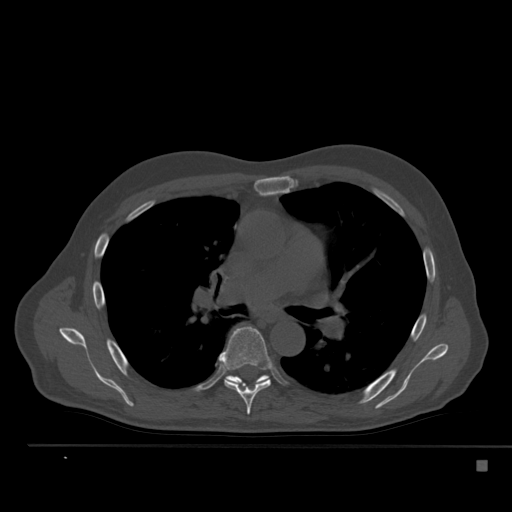
CT including the spine, one axial slice. Position 342 of 517 along the scan axis. Reconstruction kernel Br40s. 120 kVp. Bone window (W 1800 / L 400 HU). 512 × 512 image matrix. Patient: male, 70 years. From the clinical record (not read from this slice): primary cancer: renal; vertebrae with lytic lesions (as recorded): T4, T6, T10, T12, L3, L4, L5.
Outlined on this slice (semi-automatically segmented with operator editing):
- T6 vertebra: bounding box (x1, y1, x2, y2) in pixels: (219, 327, 272, 415)
- T7 vertebra: (225, 375, 270, 383)